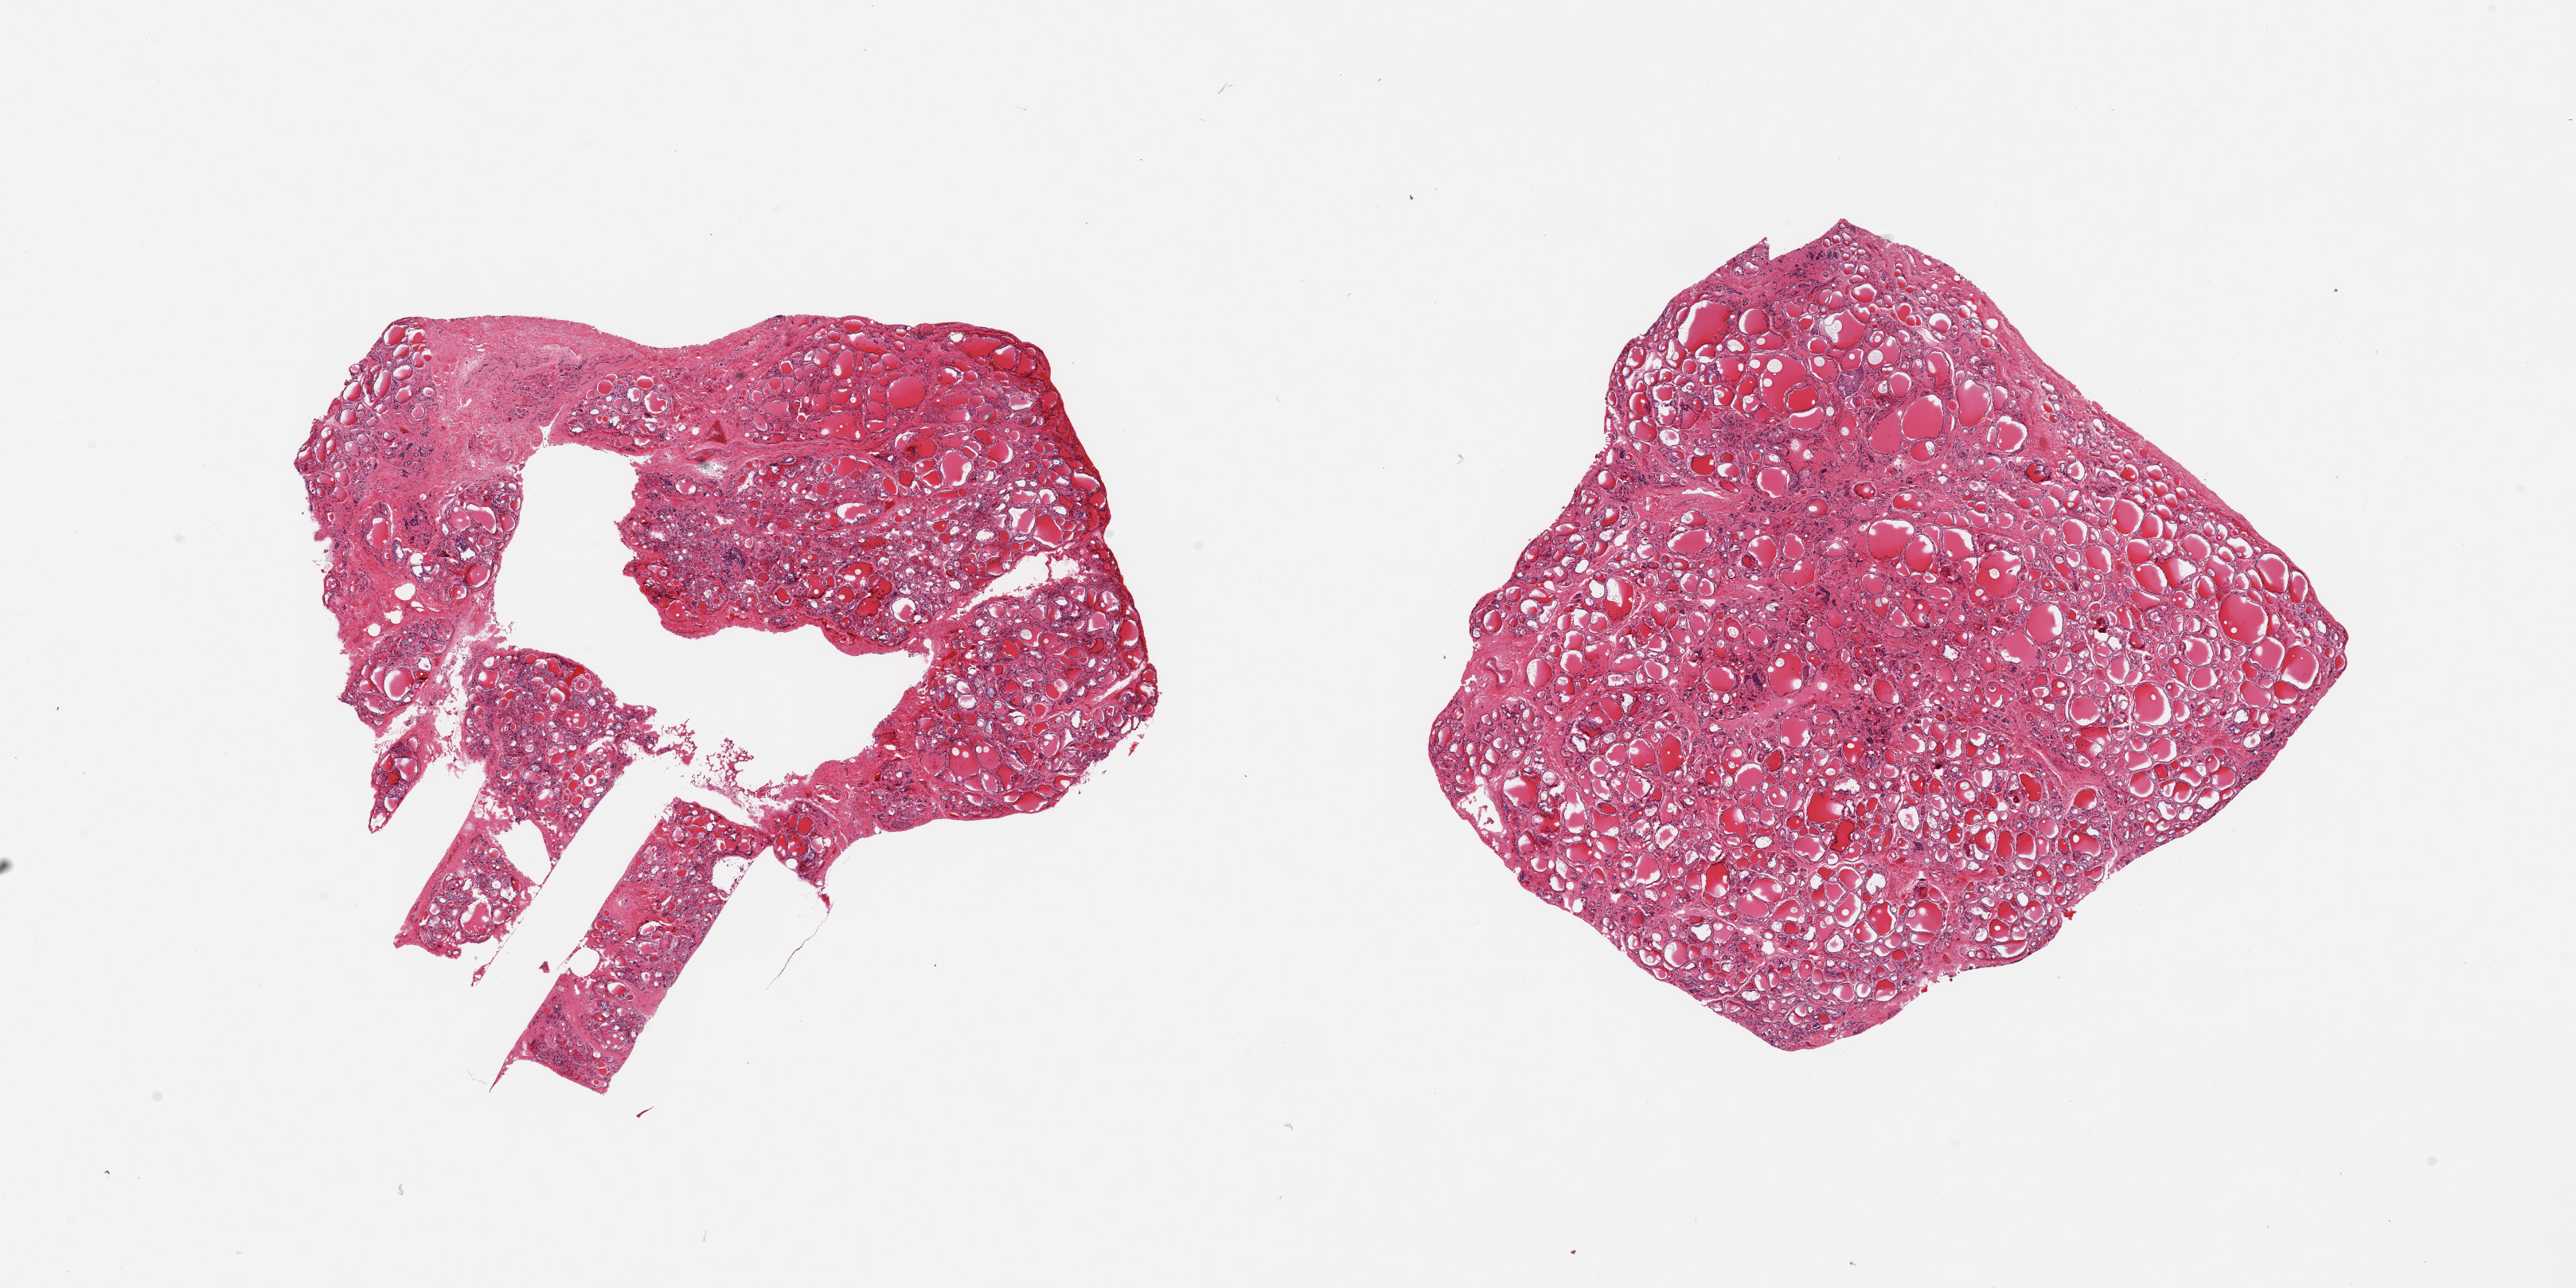
Digitized haematoxylin and eosin-stained section, low-resolution overview of the scanned area, about 25.6 x 12.8 mm, PAXgene-fixed, paraffin-embedded tissue, target tissue: thyroid, donor tissue sample. Donor: male.
• pathologist's review note for this sample: 2 pieces, no abnormalities